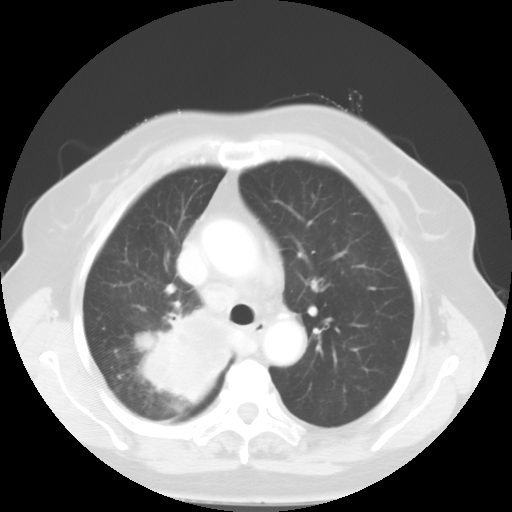
Chest CT, one axial slice; position 37 of 52 along the scan axis; reconstruction kernel STANDARD; lung window (W 1500 / L -600 HU); 512 × 512 image matrix. Female patient, age 81 years. Case-level facts recorded for this patient, not image findings: clinical TNM (as recorded): T4 N3 M1b.
Structures marked on this image (bounding box drawn by a radiologist):
- lung tumour (recorded histology: adenocarcinoma): bounding box [x1, y1, x2, y2] px = [130, 306, 241, 404]